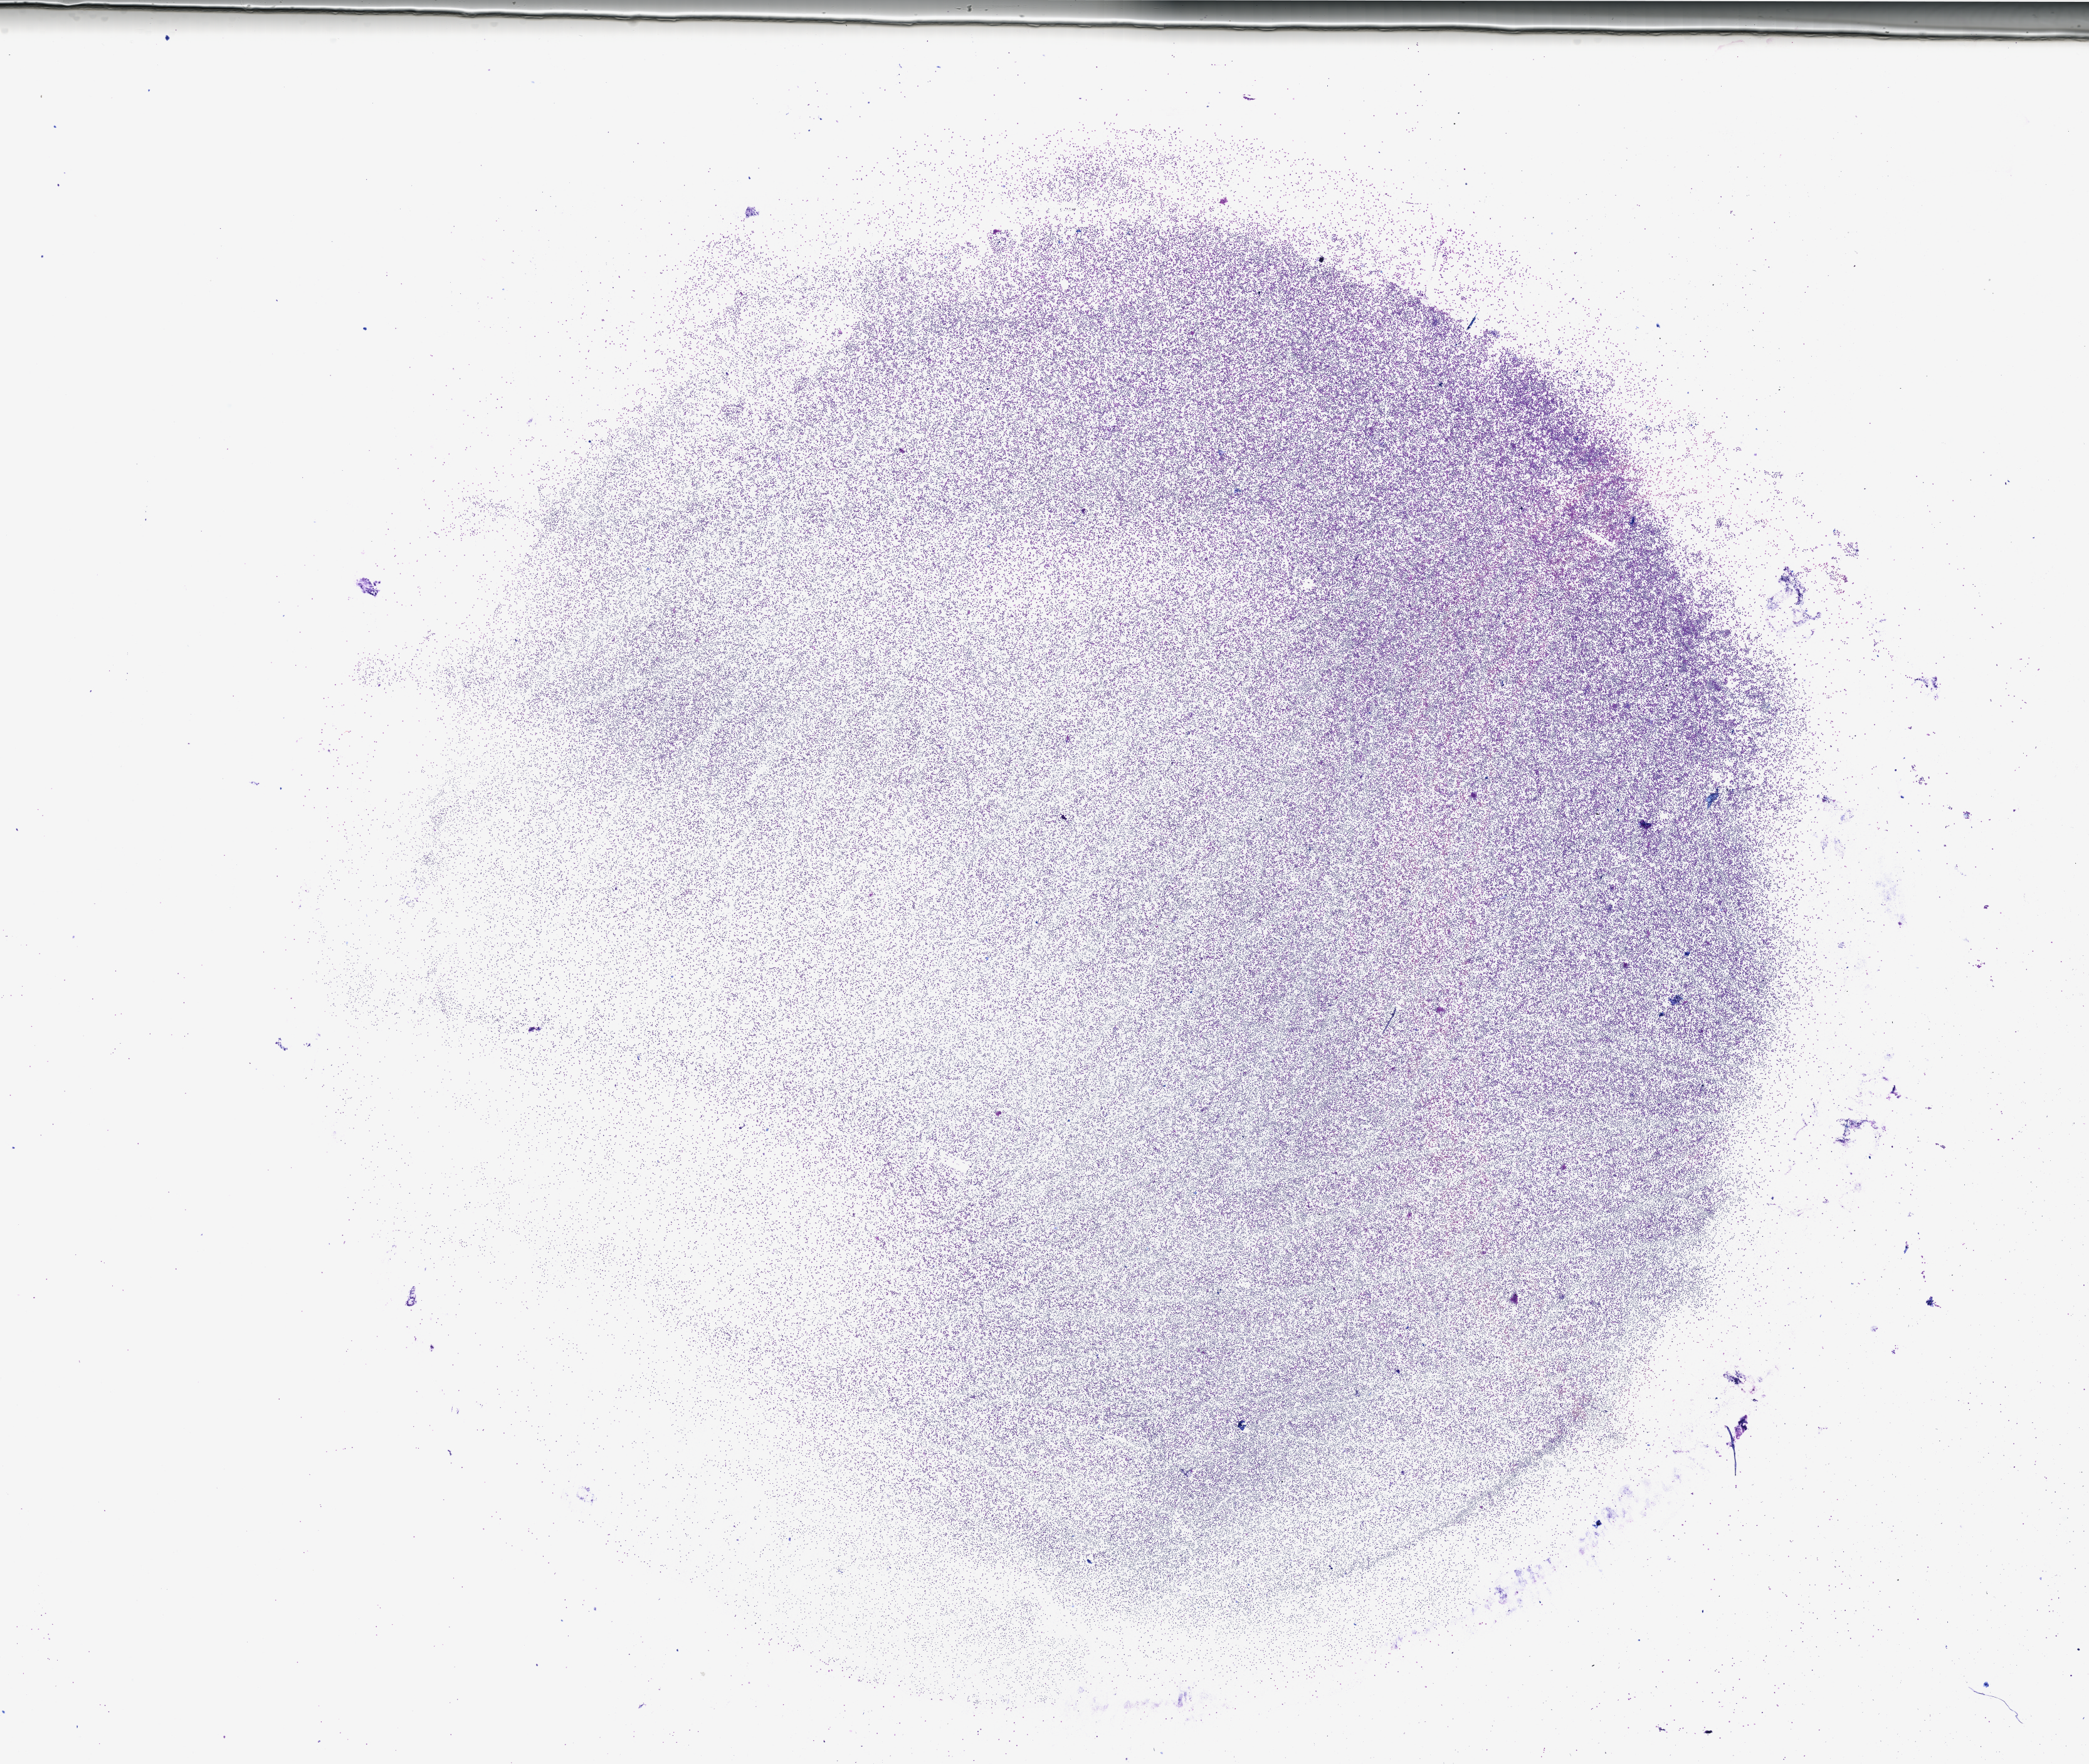
Digitized Hematoxylin and eosin (H&E) stained tissue section (whole slide), whole scanned area (about 26.3 x 22.2 mm) shown as a low-resolution overview, bone marrow (leukaemic) sample. Female, 54 y/o. Blasts: 90%.
WHO classification: AML with maturation. FAB classification: M2. Diagnosis: Acute Myeloid Leukemia.